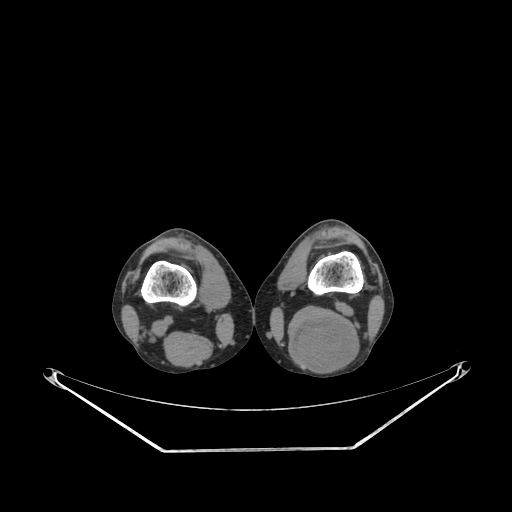
CT of an extremity soft-tissue mass (from a PET/CT study), one axial slice; slice 189 of 267 in the series (ordered by position); reconstruction kernel SOFT; 140 kVp; soft-tissue window (W 400 / L 40 HU); 3.75 mm slice thickness; 512 × 512 image matrix. Male patient. From the clinical record (not read from this slice): histological type: synovial sarcoma; site of the primary tumour: left poplietal fossa.
Outlined on this slice (expert contour drawn on MRI and transferred to this co-registered scan by the dataset authors):
- gross tumour volume (mass): bounding box <288,315,359,373> (left, top, right, bottom; pixels)